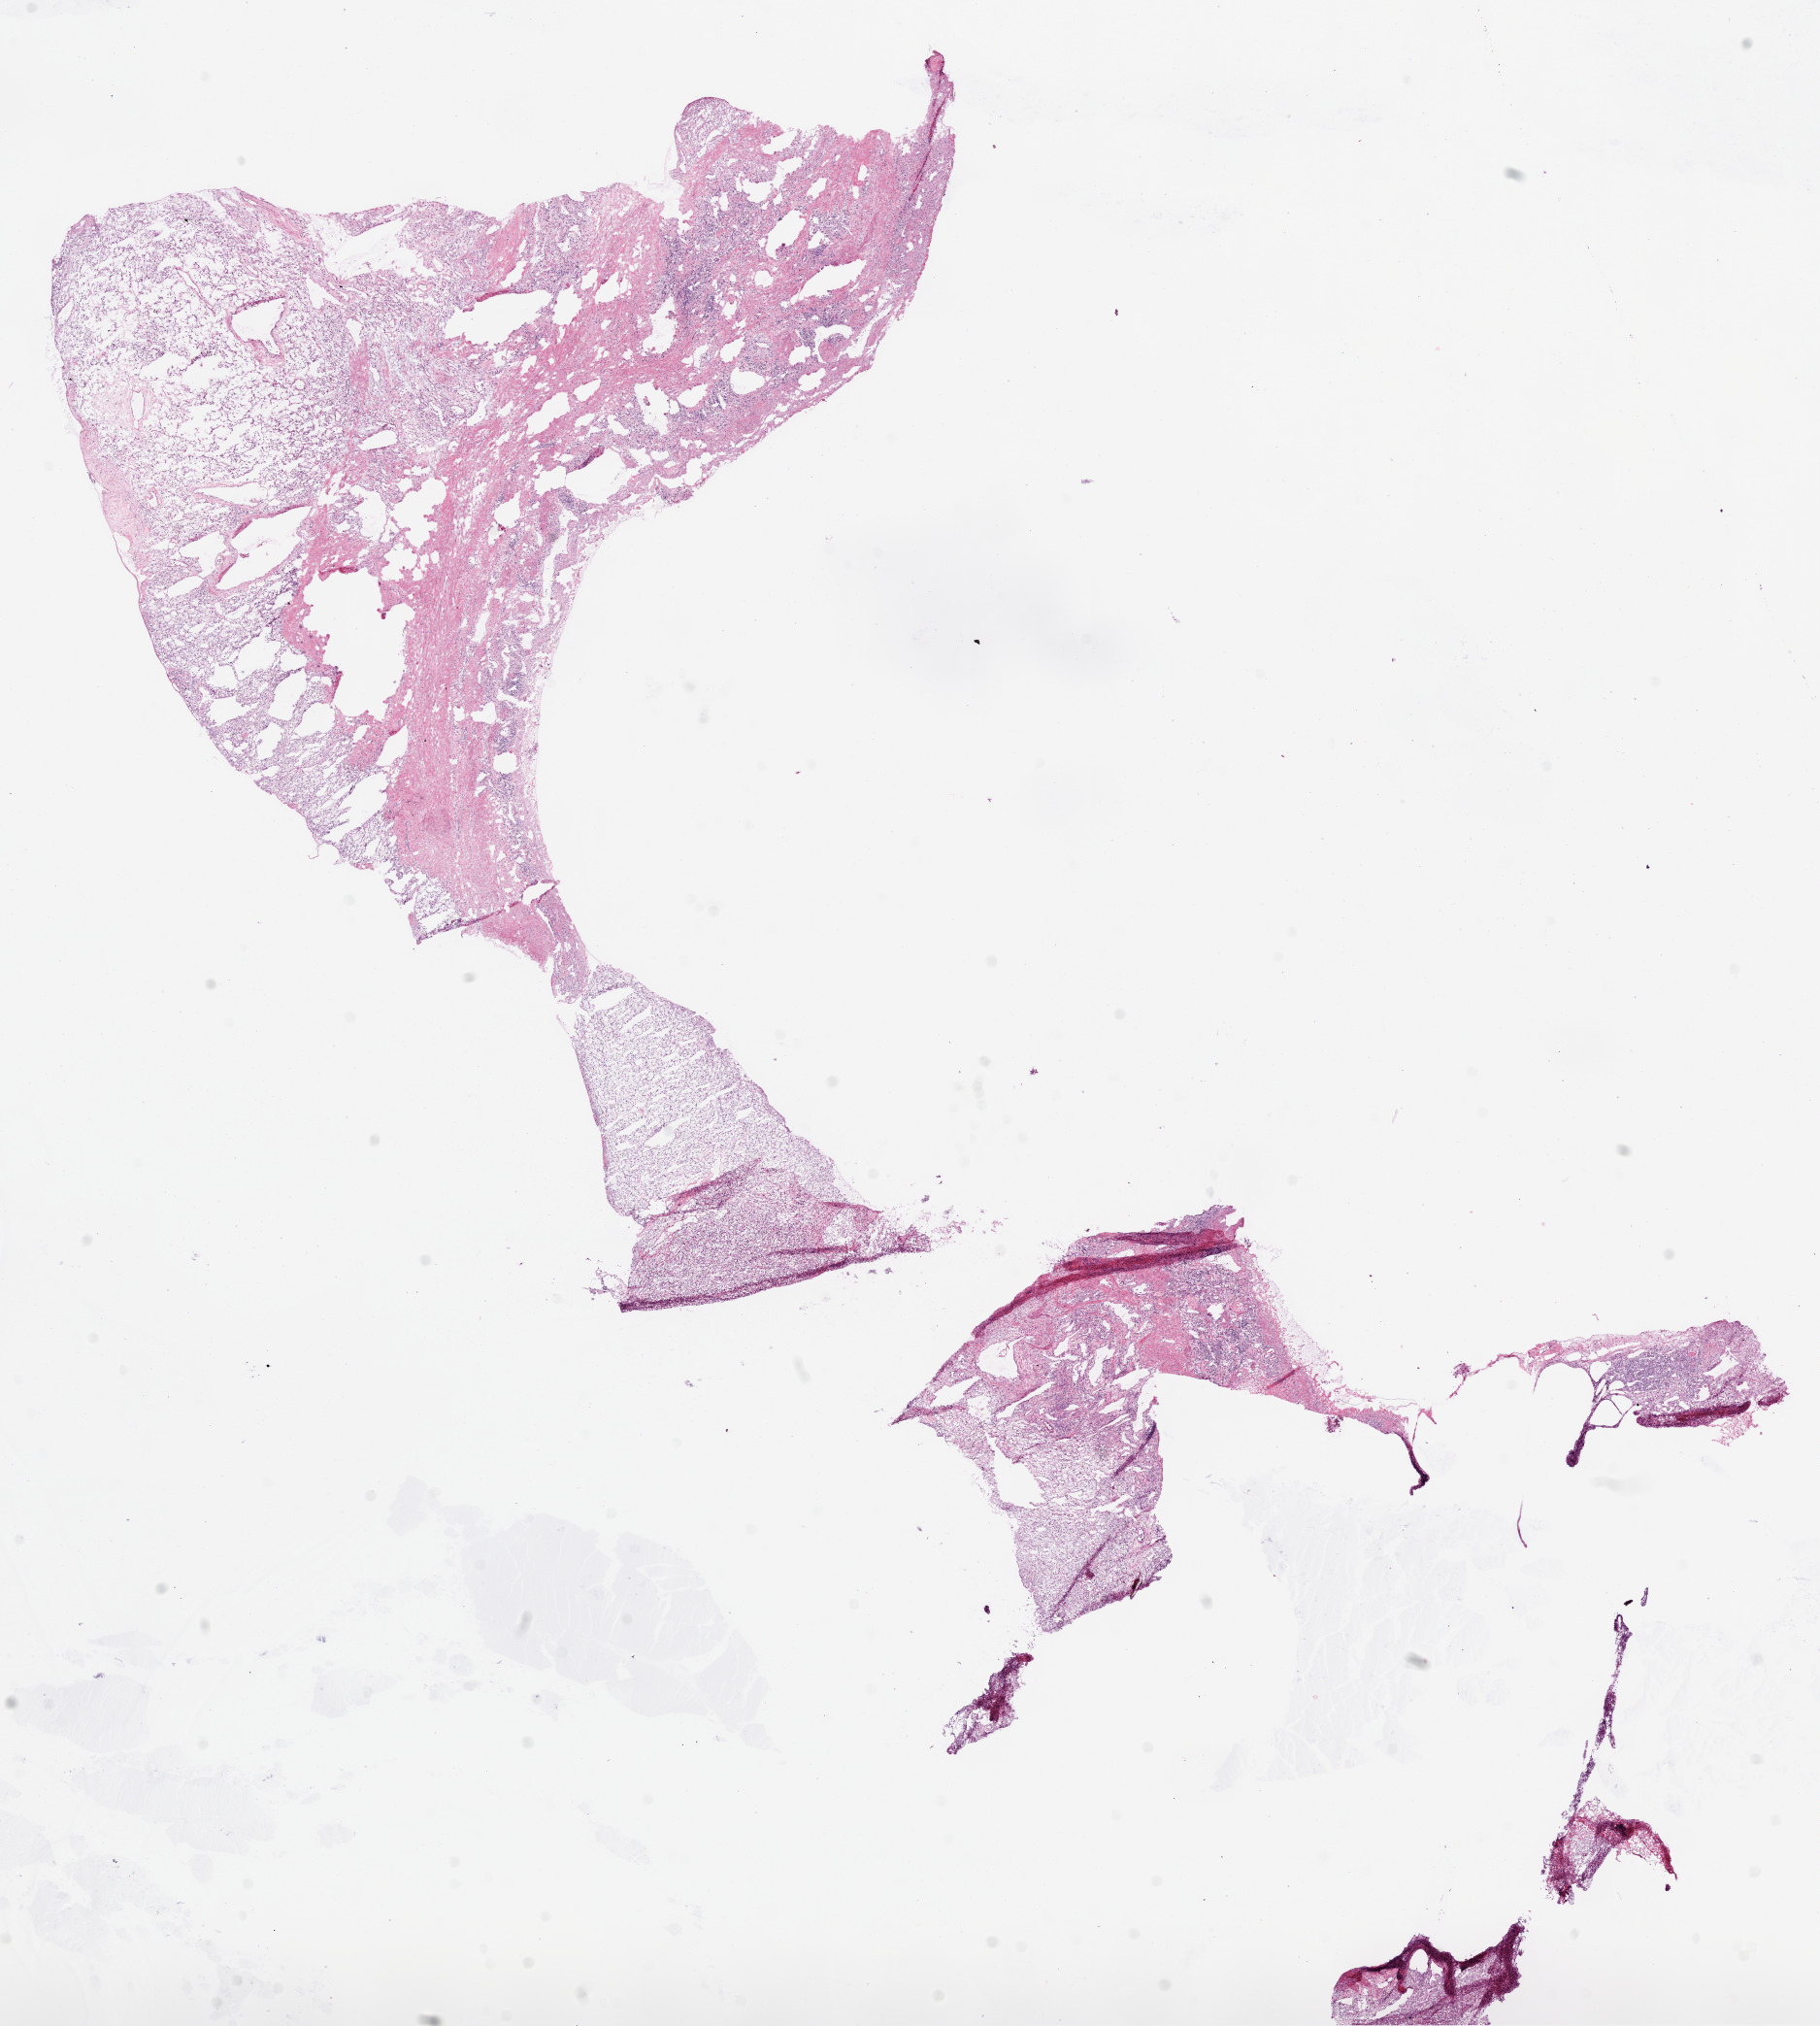
H&E-stained whole-slide image, low-resolution overview of the scanned area, about 15.0 x 16.7 mm (acquisition: 20x scan); frozen section from the bottom of the tissue portion; primary tumour sample from the kidney. Female, age 76 years at initial diagnosis. Histologic grade: G2 (moderately differentiated). Composition of this section per pathologist review: tumour cells 70%, tumour nuclei 65%, normal cells 15%, stromal cells 15%, necrosis 0%.
Laterality: right. AJCC pathologic stage: II. Histologic diagnosis: Clear cell adenocarcinoma, NOS.